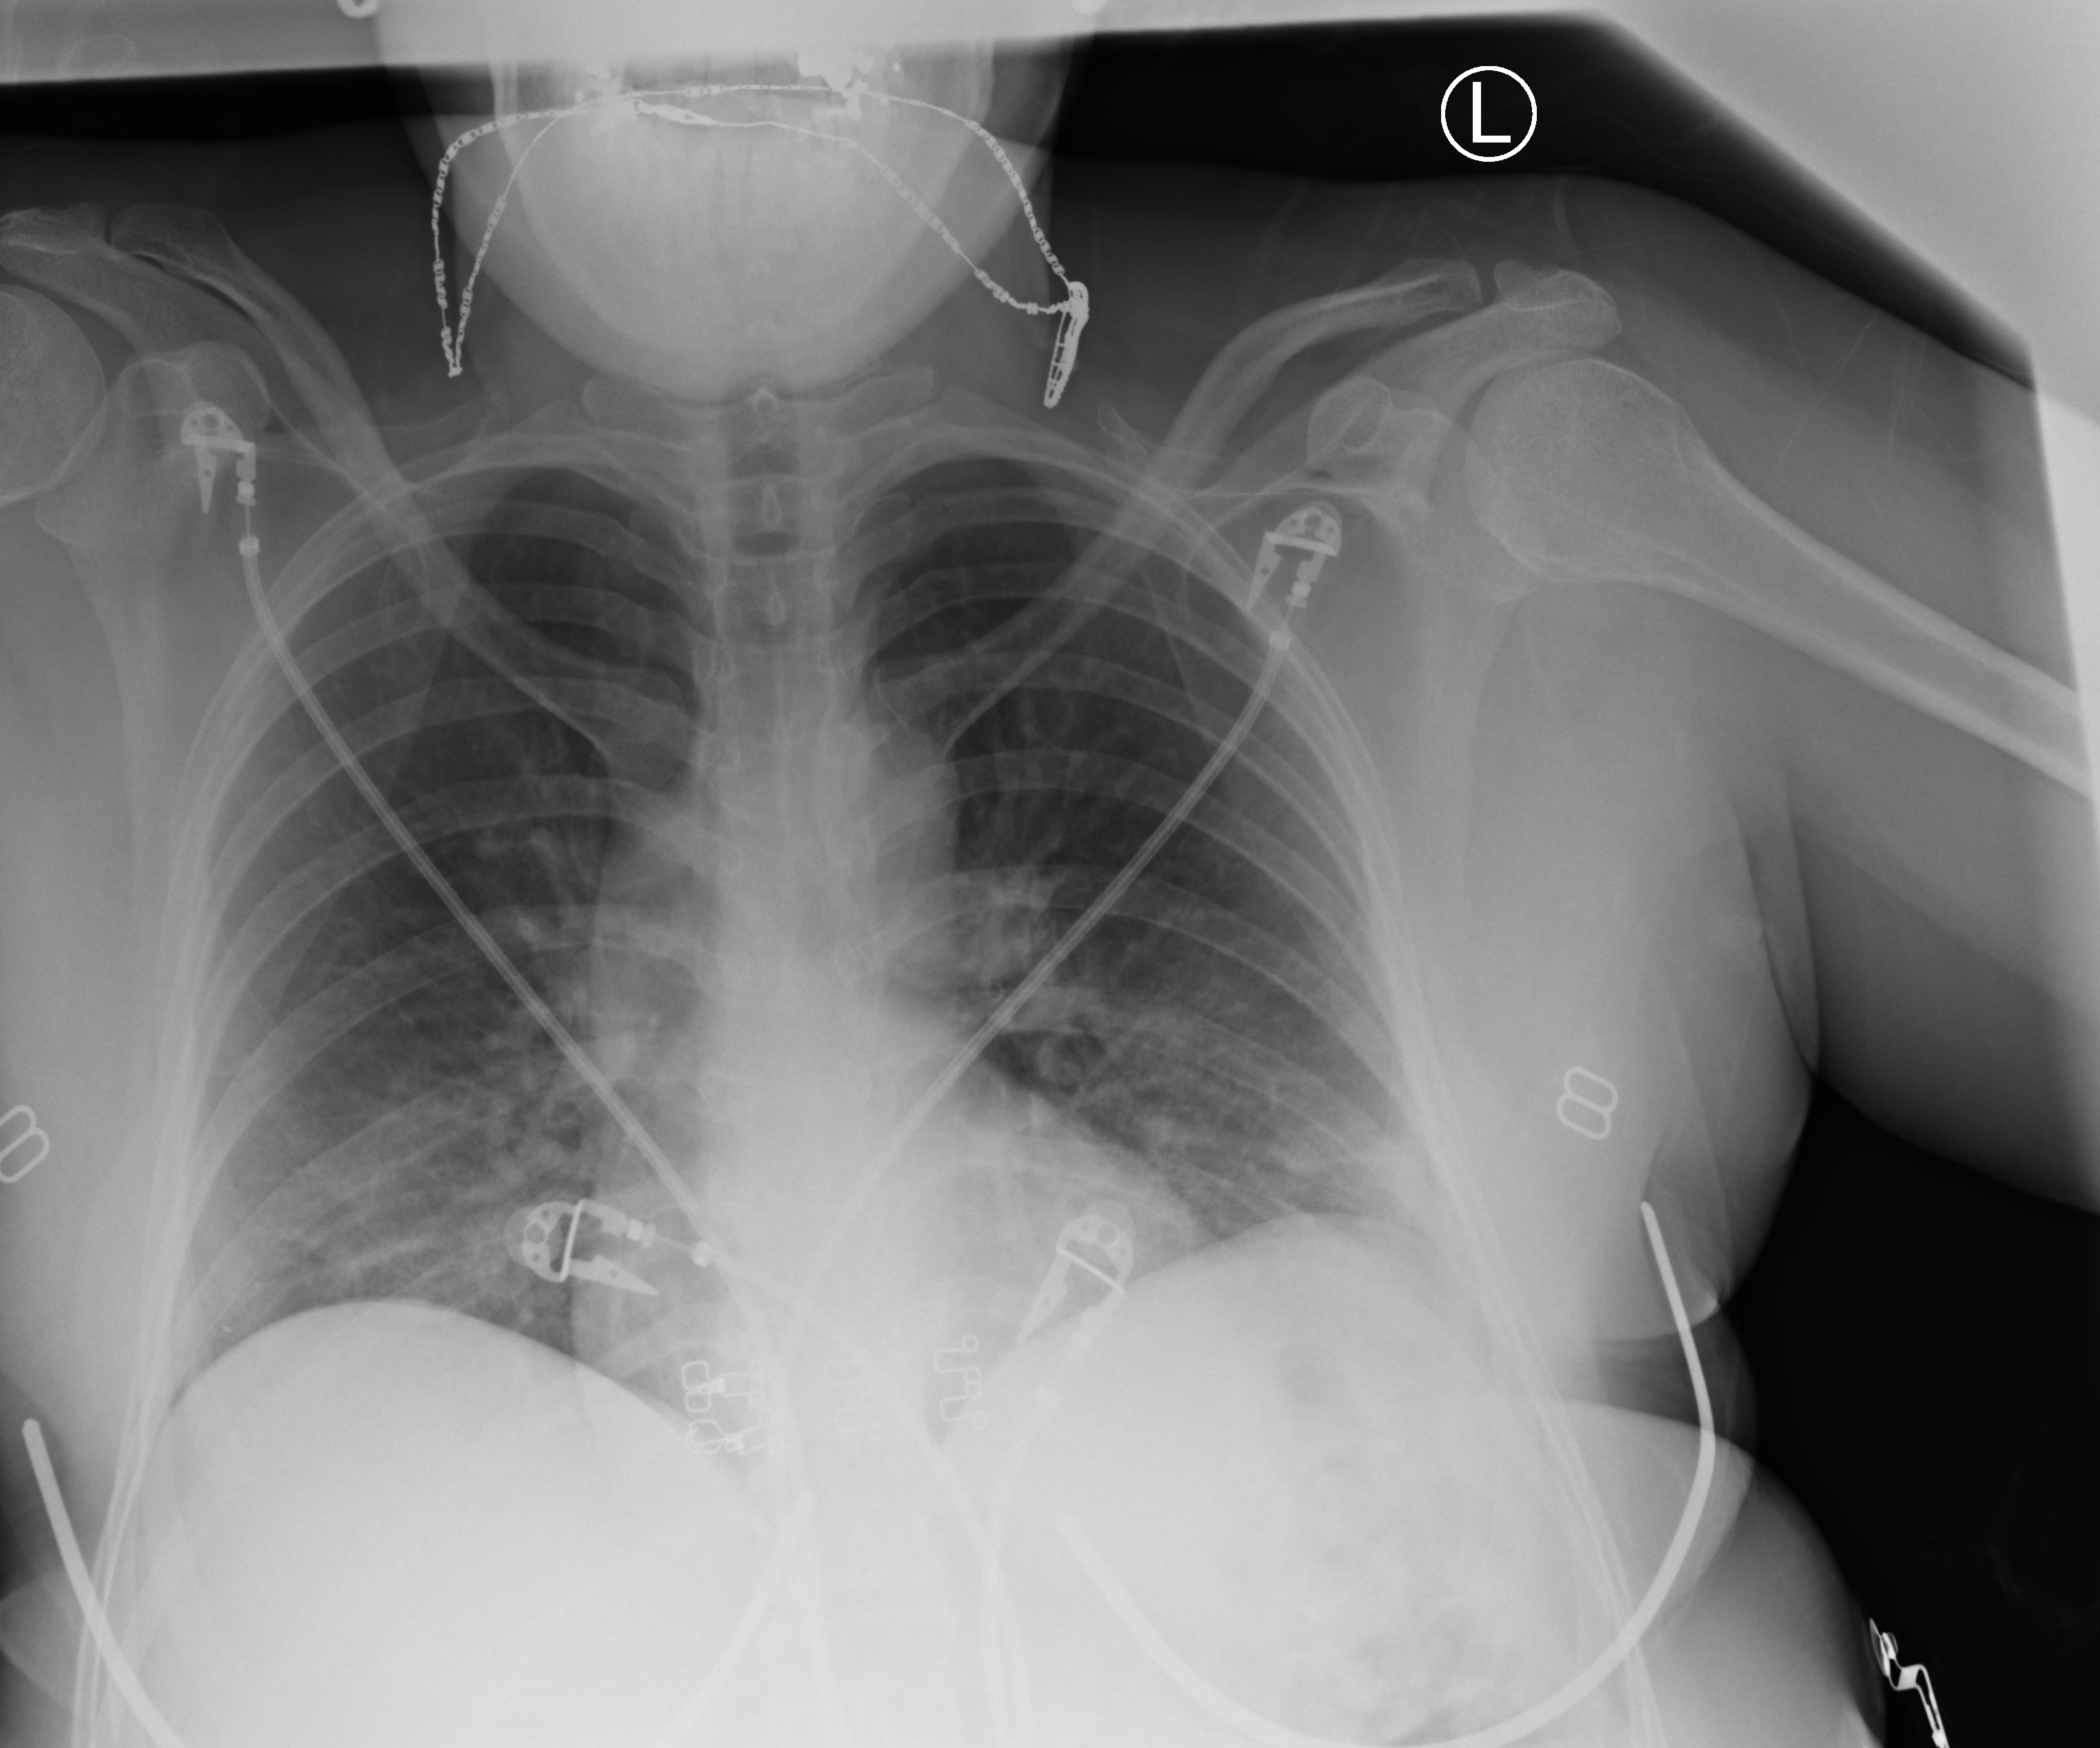
Bedside chest radiograph (computed radiography), anteroposterior (AP) projection. Patient hospitalised with COVID-19; female, aged 18–59 years.
Hospital-stay facts (about this admission, not read from this image; timing relative to this image not recorded): mechanically ventilated during this hospital stay: no; chronic kidney disease (admission record): no; admitted to intensive care during this hospital stay: no.